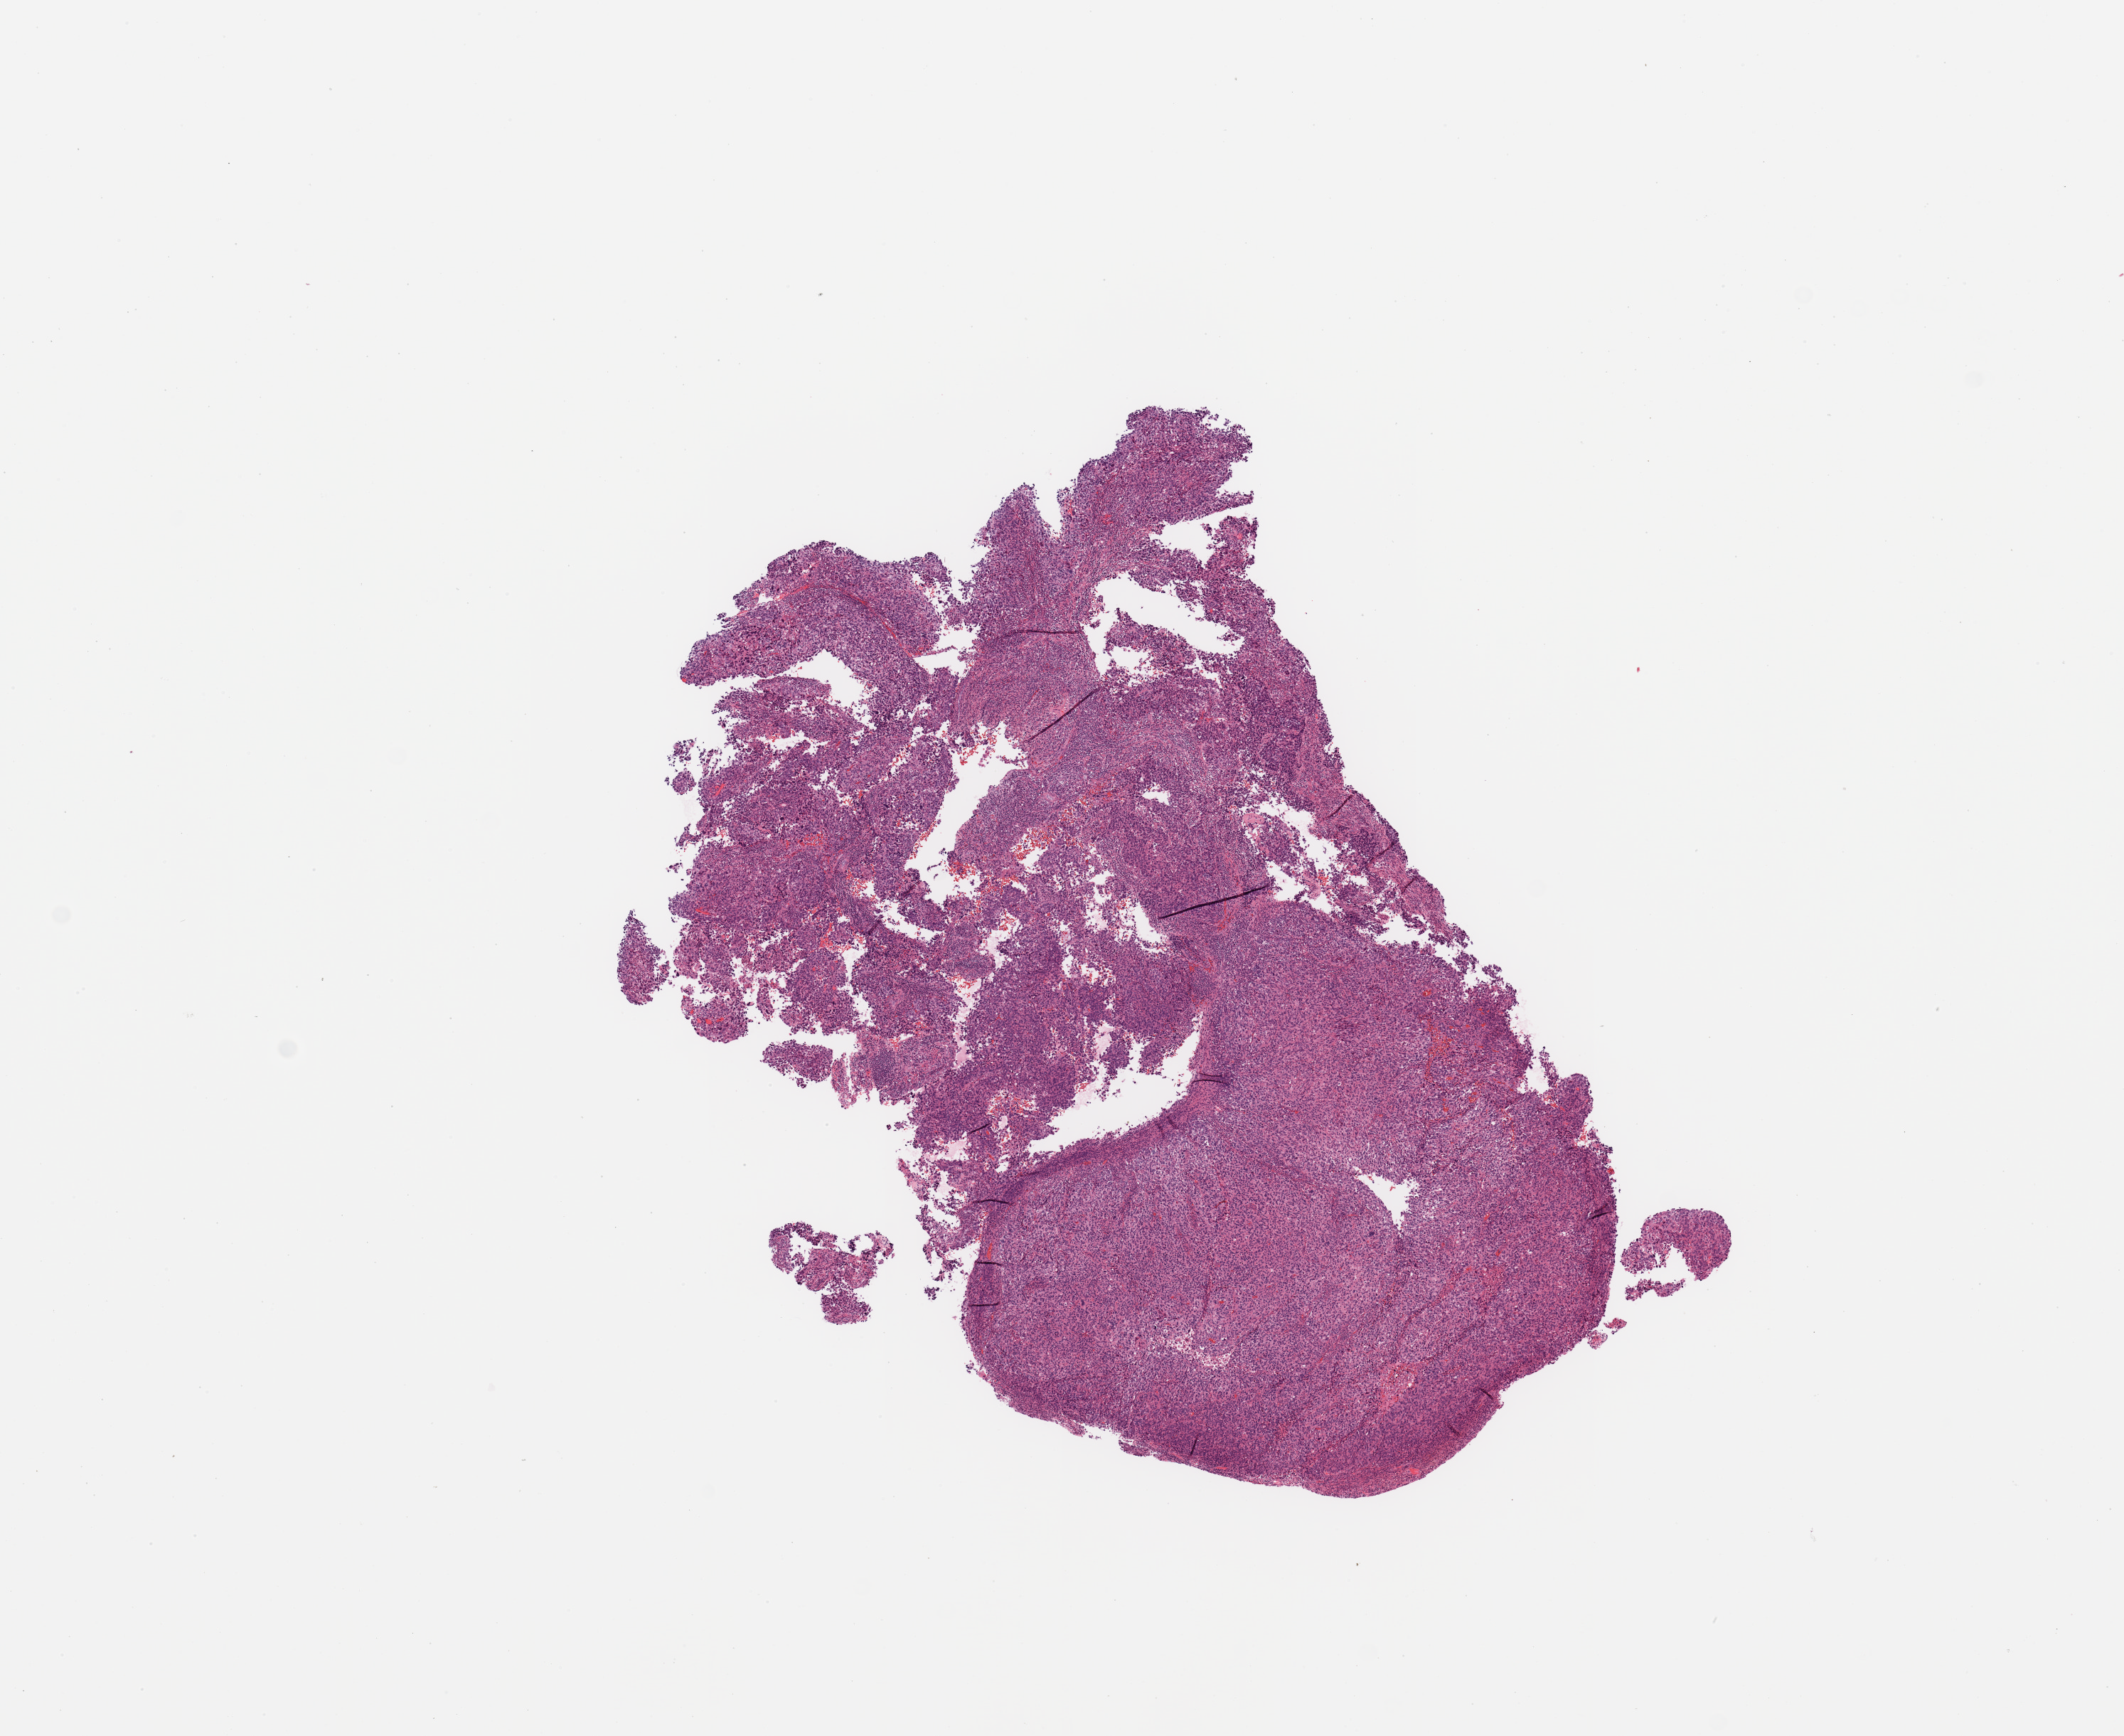
H&E-stained whole-slide image, low-resolution overview of the scanned area, about 11.8 x 9.7 mm (acquisition: 20x scan), tumour tissue sample, sampled site: uterus. Patient: female, age 60 years. Histologic grade: G3 (poorly differentiated). Composition of this section per pathologist review: tumour nuclei 98%, necrosis 0%.
Histologic diagnosis: Endometrioid adenocarcinoma, NOS. AJCC pathologic stage: I.